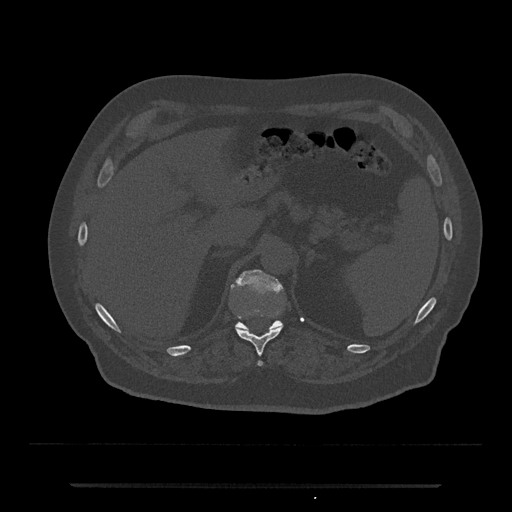
CT including the spine, one axial slice. Slice 631 of 797 in the series (ordered by position). Bone window (W 1800 / L 400 HU). 0.5 mm slice thickness. 512 × 512 image matrix, field of view 434 × 434 mm. Male patient, age 80 years. From the clinical record (not read from this slice): primary cancer: prostate; vertebrae with lytic lesions (as recorded): L1, T11.
Structures marked on this image (semi-automatically segmented with operator editing):
- T11 vertebra: bounding box (x1, y1, x2, y2) in pixels: (236, 327, 282, 366)
- T12 vertebra: (231, 269, 283, 331)